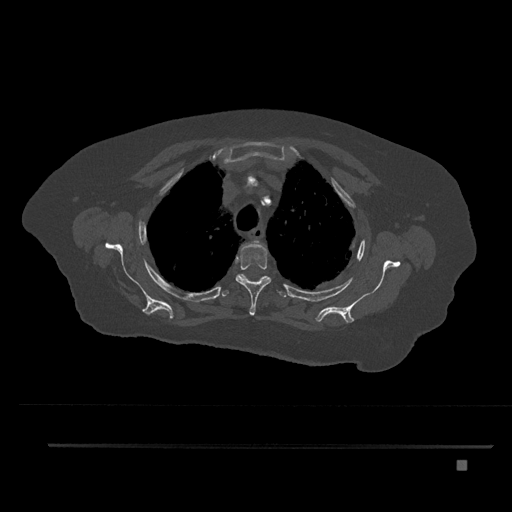
CT including the spine, one axial slice; slice 632 of 797 in the series (ordered by position); bone window (W 1800 / L 400 HU); 512 × 512 image matrix, field of view 437 × 437 mm. Patient: female, 76 years. From the clinical record (not read from this slice): primary cancer: lung; vertebrae with lytic lesions (as recorded): T11, L3.
Outlined on this slice (semi-automatically segmented with operator editing):
- T2 vertebra: bounding box <254,240,261,244> (left, top, right, bottom; pixels)
- T3 vertebra: <235,243,272,316>
- T4 vertebra: <222,274,286,298>